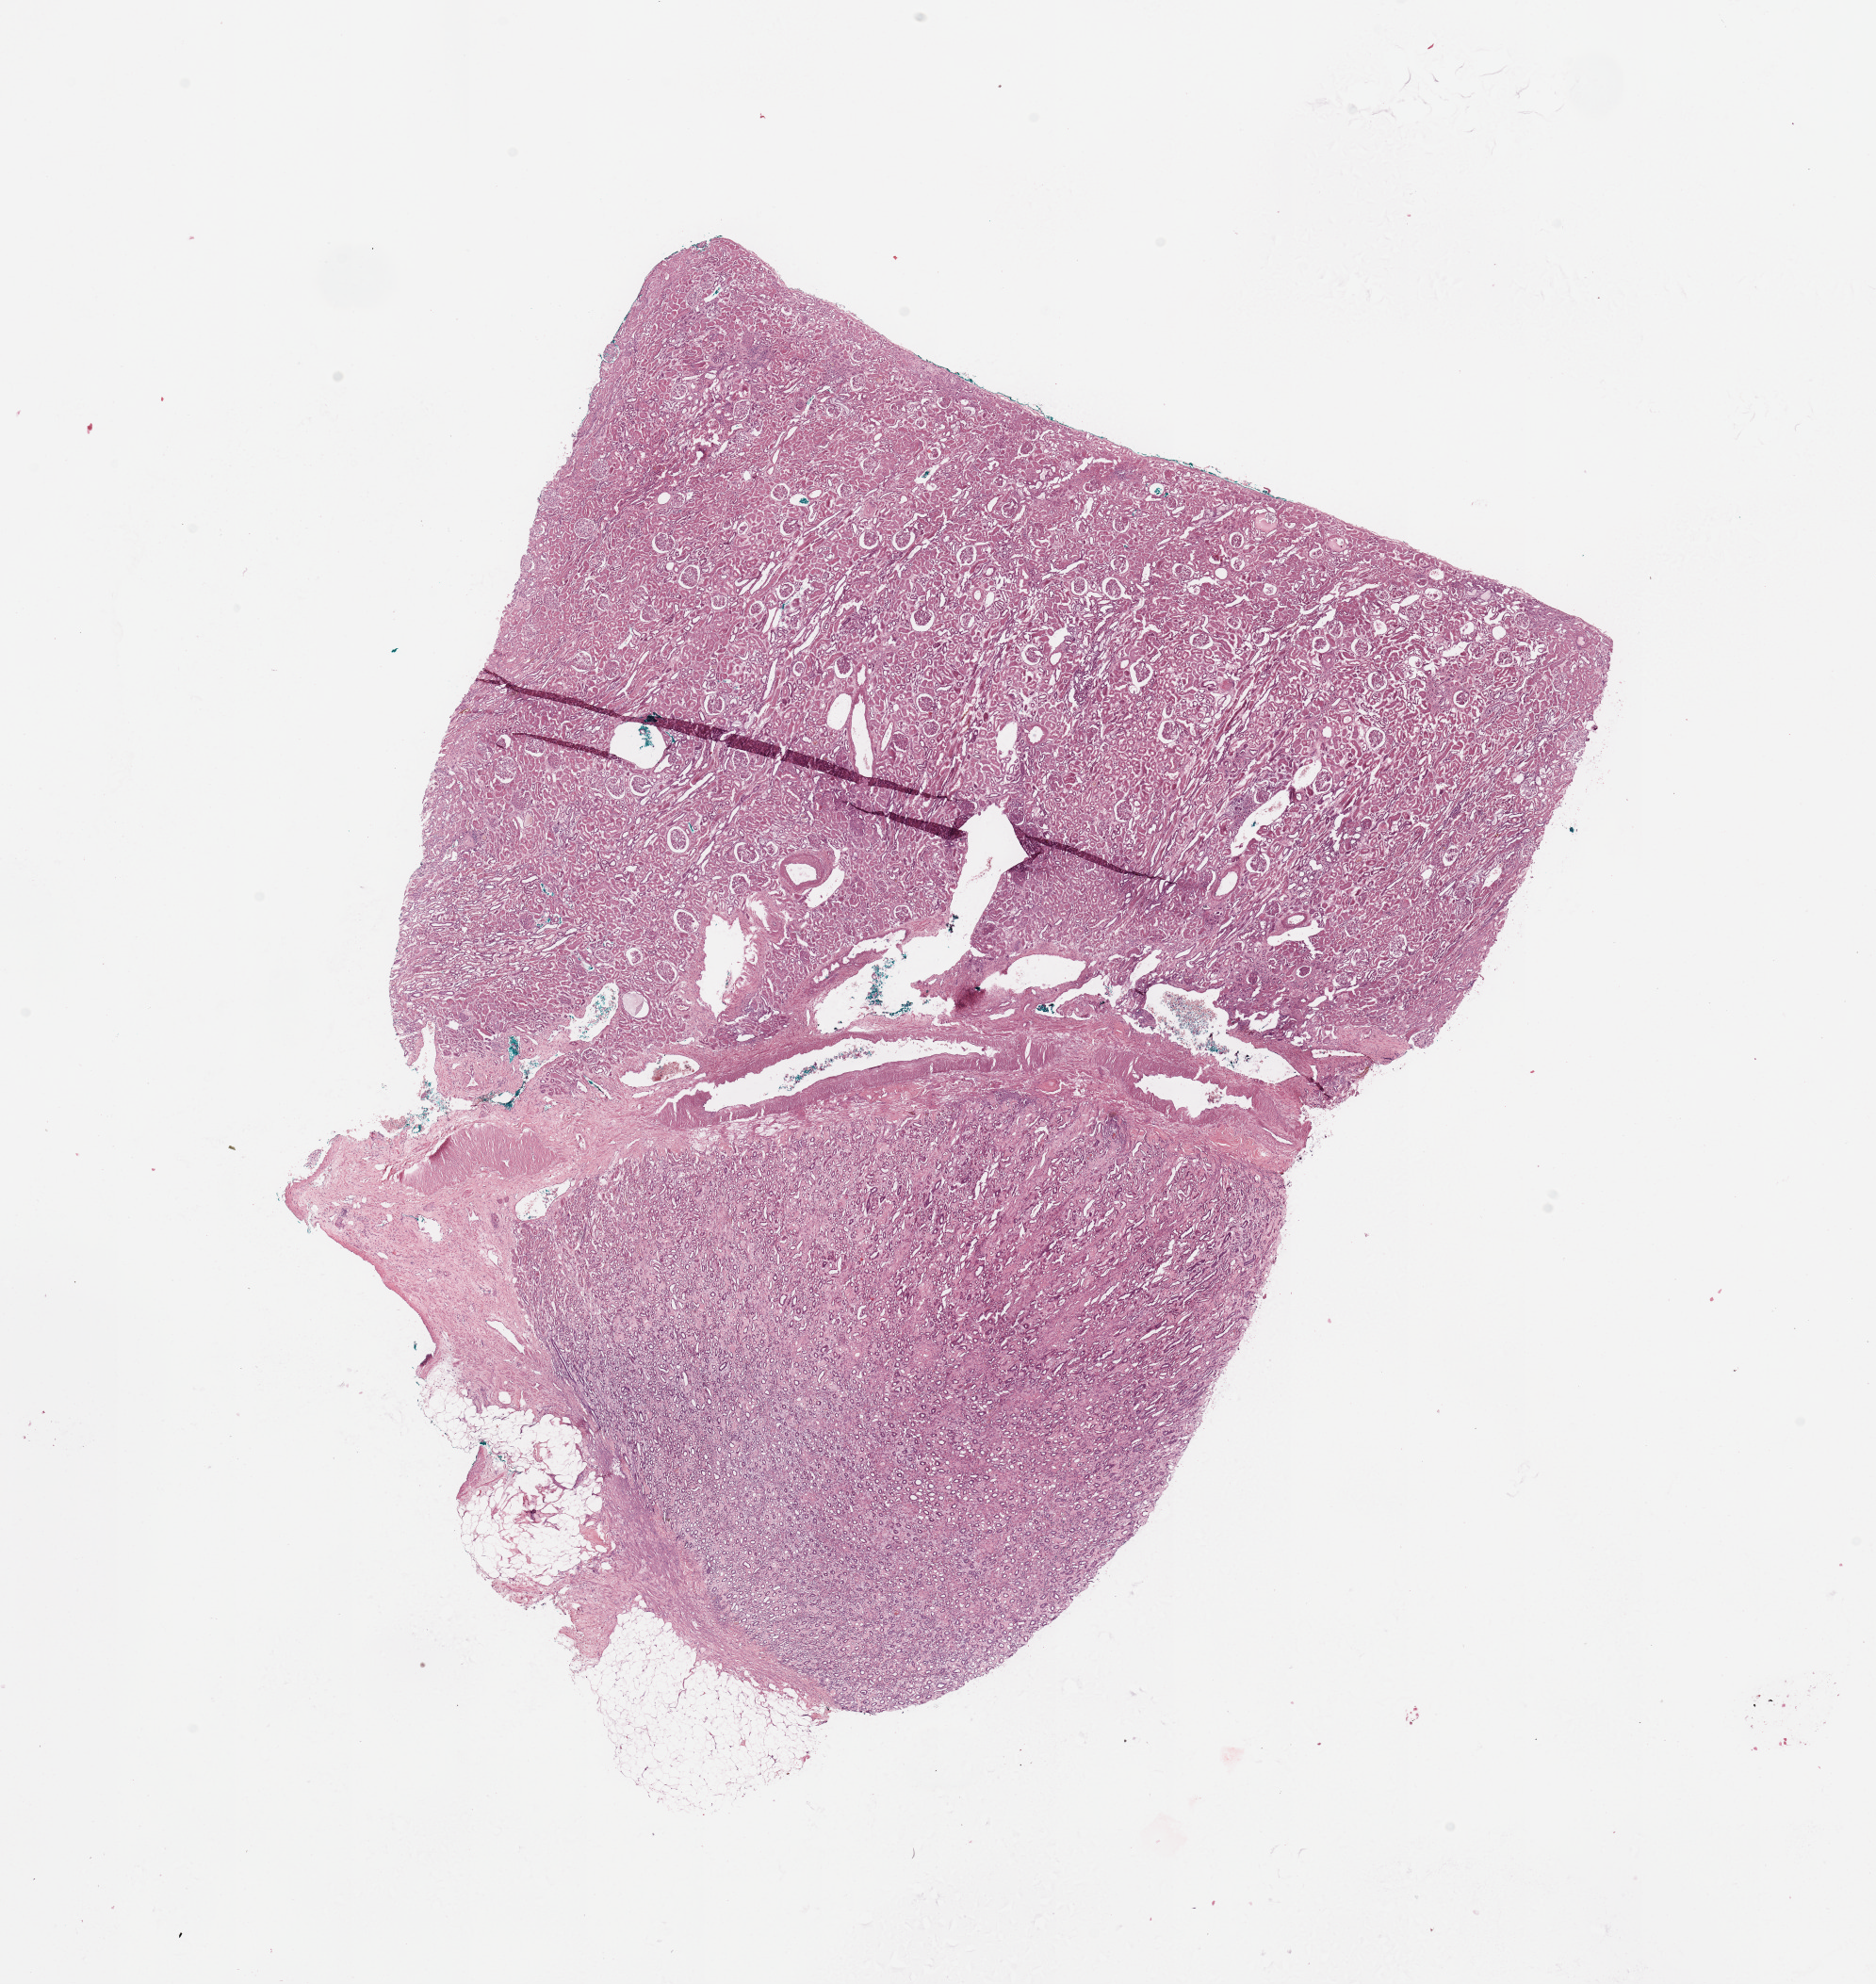
H&E-stained whole-slide image — shown as a low-resolution overview of the whole scanned area (about 15.8 x 16.7 mm); normal (non-tumour) tissue sample, kidney. Patient: male, age 45 years.
This section: normal (non-tumour) tissue from the same patient. Patient diagnosis: Renal cell carcinoma, NOS.